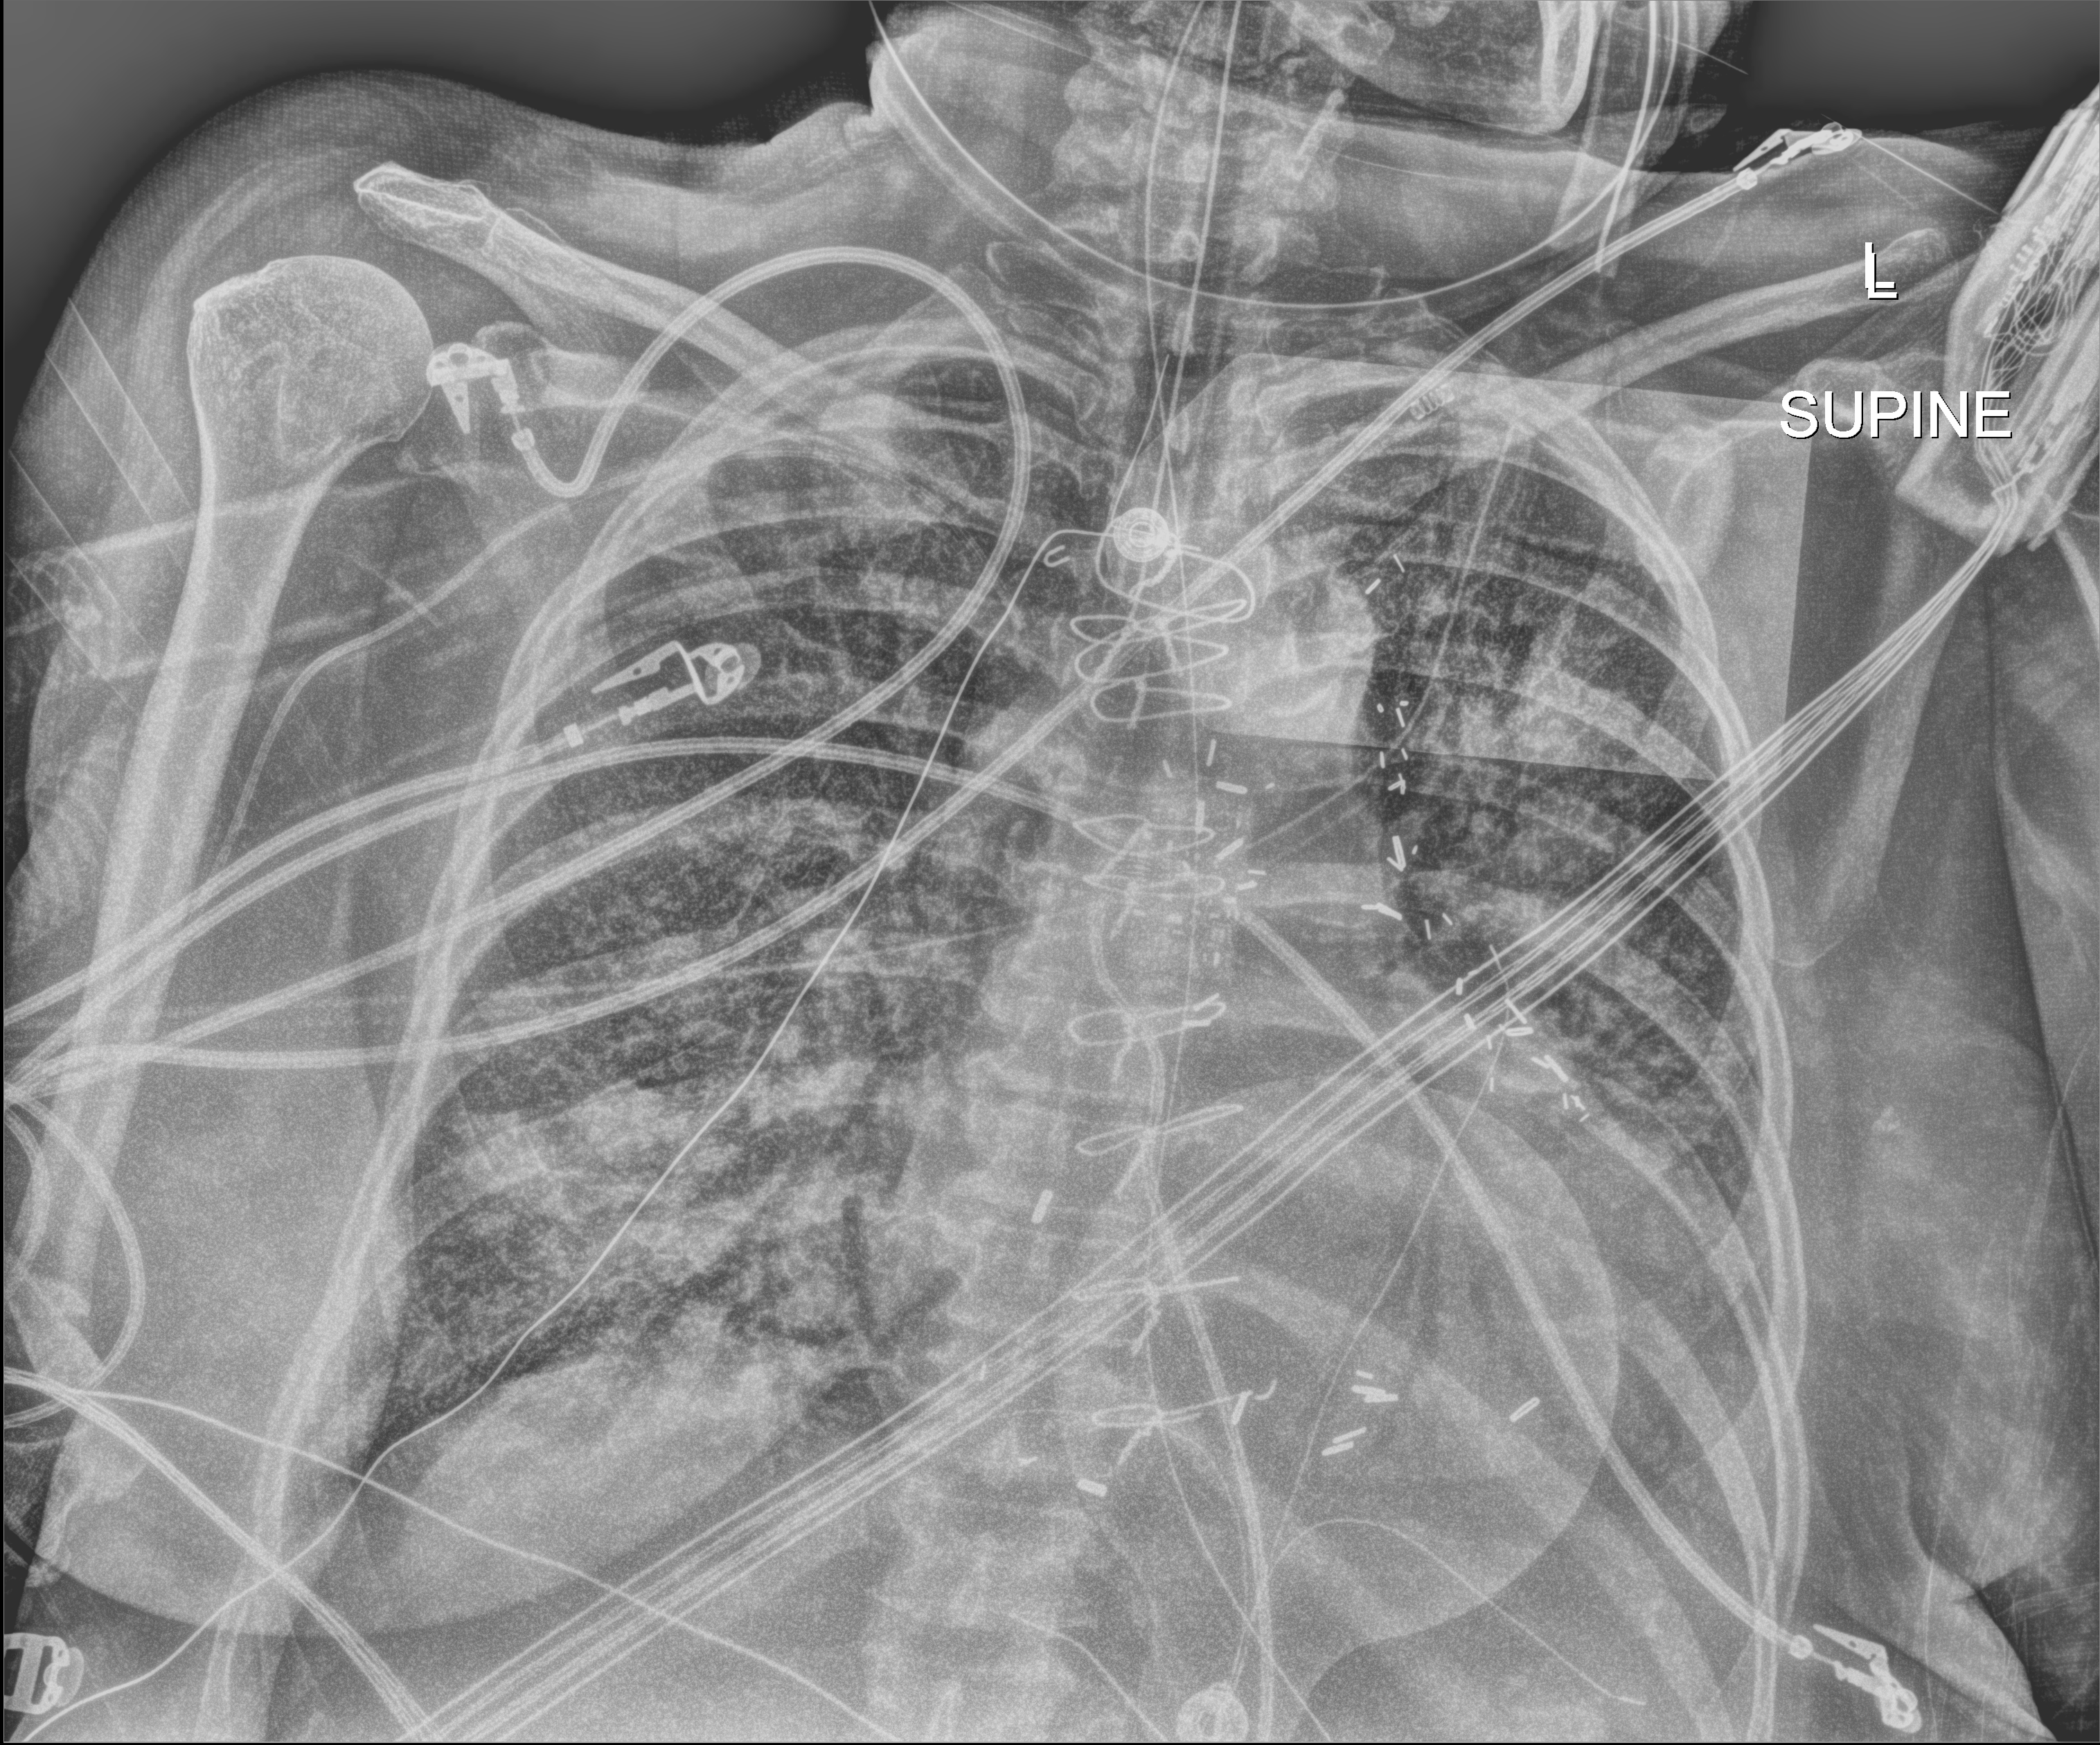
Bedside chest radiograph (digital radiography); anteroposterior (AP) projection. Patient hospitalised with COVID-19; female, aged 60–74 years.
From the hospital-stay record, not from the radiograph (when in the stay this image was taken is not recorded): diabetes (admission record): no; mechanically ventilated during this hospital stay: yes.